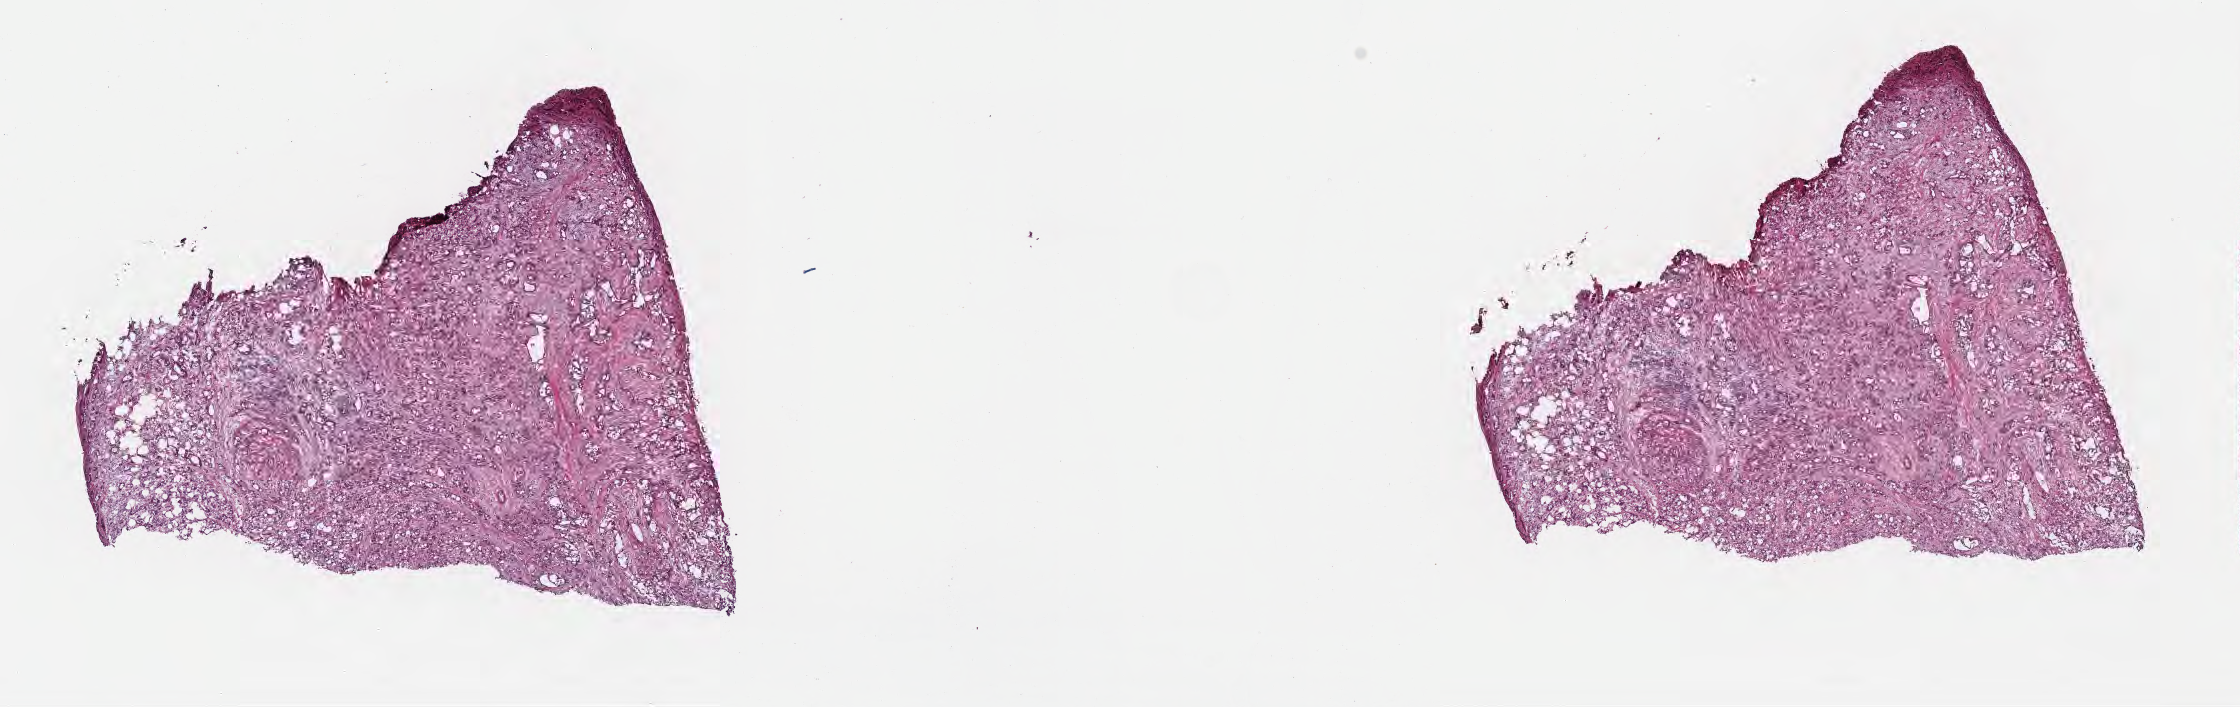
Digitized hematoxylin and eosin (H&E)-stained section — shown as a low-resolution overview of the whole scanned area (about 18.1 x 5.7 mm). Frozen section. Primary tumor. Site: head of pancreas. Patient: male, age at initial diagnosis 62 years. Tumor grade: G3 (poorly differentiated). Composition of this section per pathologist review: tumor cells 40%, tumor nuclei 90%, stromal cells 60%, necrosis 0%, normal cells 0%. Infiltration values recorded for this section: lymphocyte infiltration 0%, monocyte infiltration 0%, neutrophil infiltration 0%.
• histologic diagnosis: Infiltrating duct carcinoma, NOS
• AJCC pathologic stage: Stage III